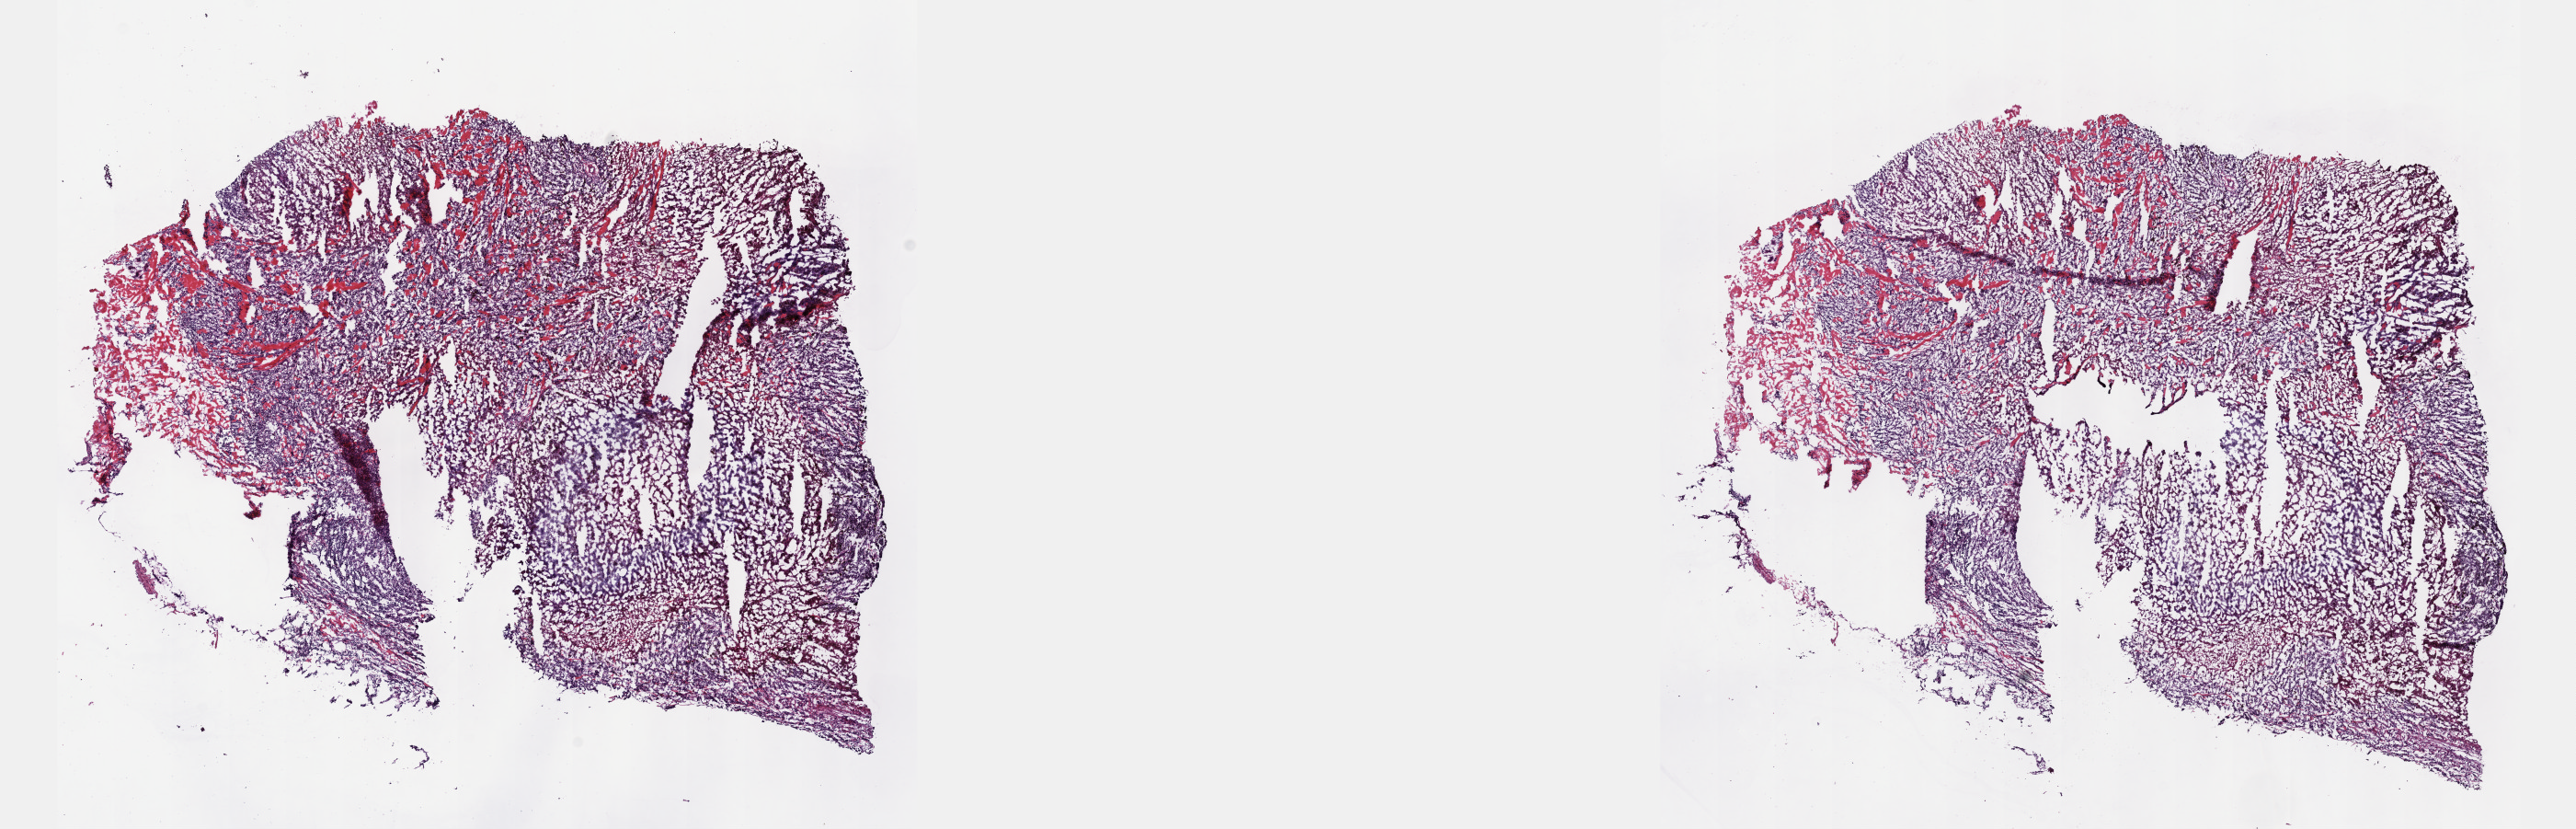
Whole-slide histology image, H&E-stained — whole scanned area (about 22.6 x 7.3 mm) shown as a low-resolution overview. Frozen section. Sample: primary tumour, skin. Female, age 76 years at initial diagnosis. Composition of this section per pathologist review: tumour cells 100%, tumour nuclei 75%, normal cells 0%, stromal cells 0%, necrosis 0%. Infiltration values recorded for this section: lymphocyte infiltration 3%, monocyte infiltration 0%, neutrophil infiltration 0%.
Histologic diagnosis: Malignant melanoma, NOS. AJCC pathologic stage: IIIC (7th edition).